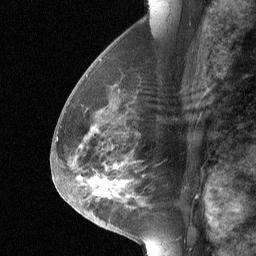
Breast MRI (dynamic contrast-enhanced), one sagittal slice; position 32 of 64 along the scan axis; dynamic contrast-enhanced study with each time point stored as its own series, time point 2 of 3 at this slice position (early post-contrast, ordered by acquisition time); 1.5 T; TE 4.8 ms, TR 27 ms; 2 mm slice thickness; 256 × 256 image matrix. Patient: female, 56 years. Case-level facts recorded for this patient, not image findings: setting: breast cancer imaged before/during neoadjuvant chemotherapy; receptor status: HER2-positive.
Annotated regions visible in this slice (semi-automatically segmented with operator editing):
- analysis volume of interest (the breast-tissue region the enhancement analysis was run in; not a lesion): bounding box <68,83,153,214> (left, top, right, bottom; pixels)
- tumour enhancement mask (voxels above the 90 % enhancement threshold inside the analysis volume of interest): <89,127,127,195>